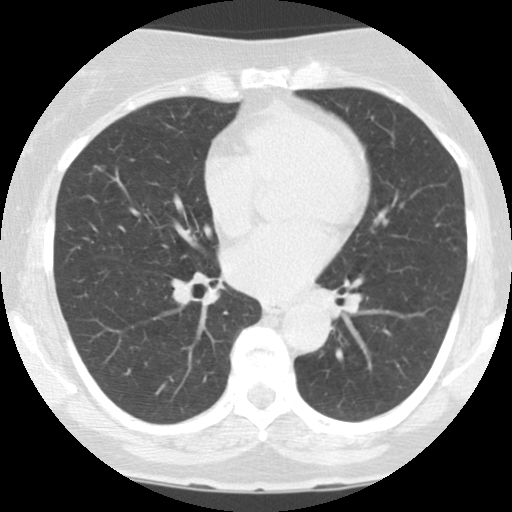
Axial slice from a low-dose chest CT screening exam; baseline annual screen; lung window (W 1500 / L -600 HU); 2.5 mm slice thickness; slice 60 of 123 in the series. Female participant, aged 60 years at enrolment.
- Expert reader's lesion annotation, bounding box <89,158,113,180> (left, top, right, bottom; pixels).
- The screening reader recorded 3 non-calcified nodules or masses ≥4 mm on this exam (left upper lobe, right upper lobe, right upper lobe); which of them this box marks is not recorded.
- Official screen result: positive, change unspecified: nodule(s) >= 4 mm or enlarging nodule(s), mass(es), or other non-specific abnormalities suspicious for lung cancer.